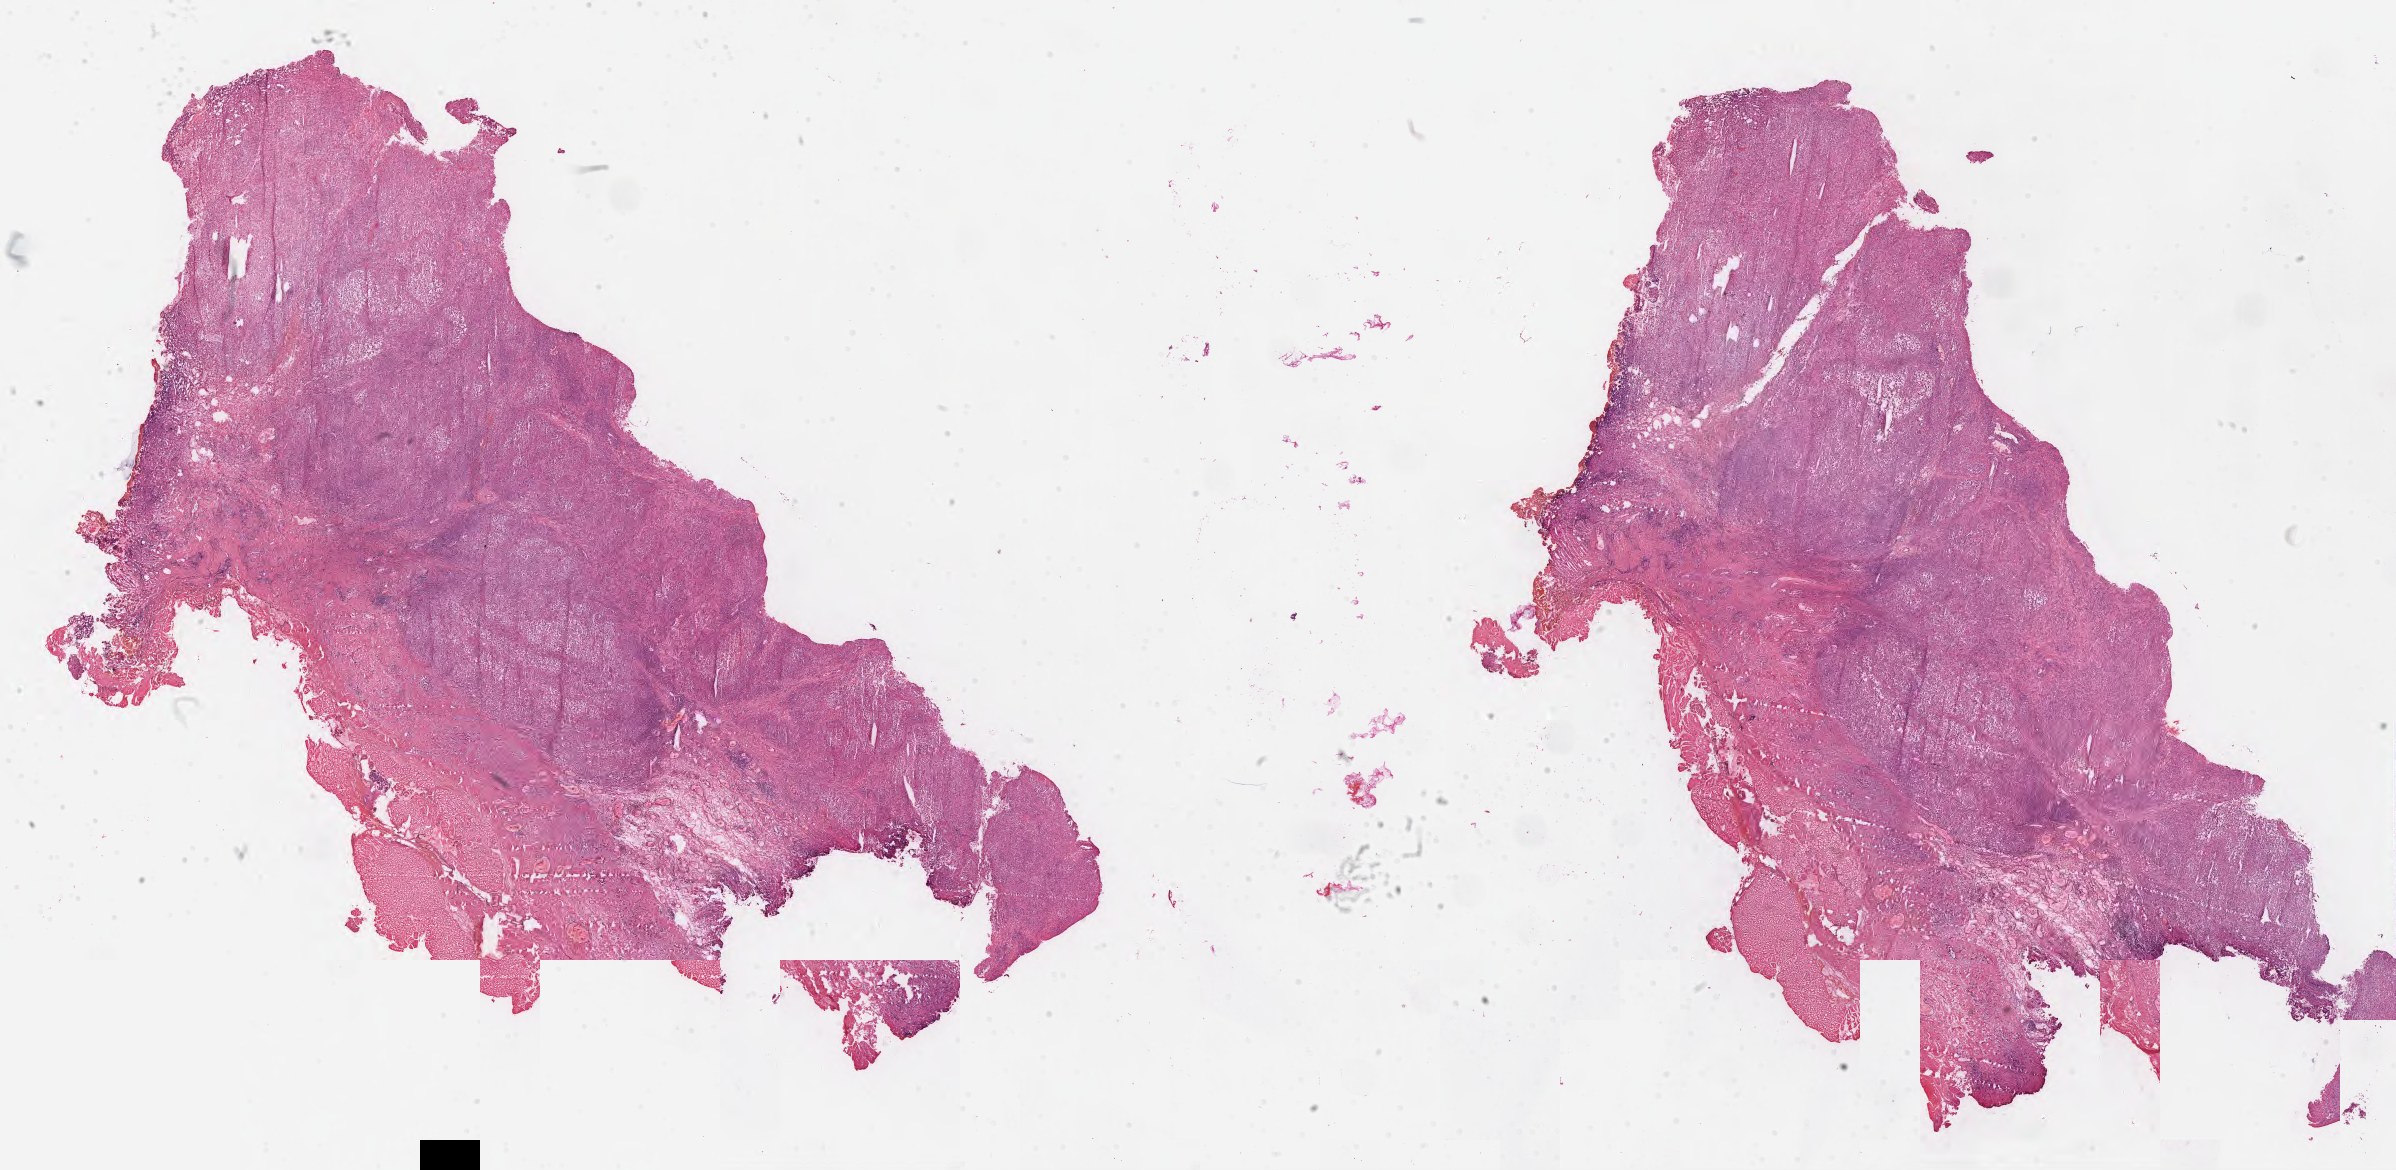
Whole-slide histology image, H&E — shown as a low-resolution overview of the whole scanned area (about 38.7 x 18.9 mm), formalin-fixed paraffin-embedded (FFPE) diagnostic section, primary tumour sample from the mesothelium. Male, age 58 years at initial diagnosis.
Laterality: right. AJCC pathologic stage: III. Pathologic diagnosis: Epithelioid mesothelioma, malignant (pleura, NOS).